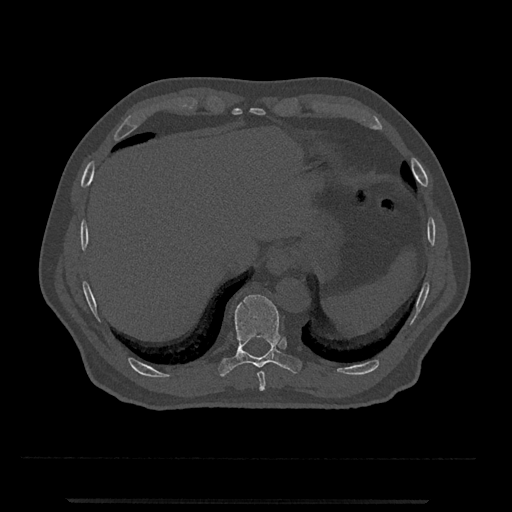
CT including the spine, one axial slice; position 526 of 797 along the scan axis; bone window (W 1800 / L 400 HU); 0.5 mm slice thickness; 512 × 512 image matrix, field of view 419 × 419 mm. Patient: male, 63 years. Case-level facts recorded for this patient, not image findings: primary cancer: prostate.
Outlined on this slice (semi-automatically segmented with operator editing):
- T10 vertebra: bounding box [x1, y1, x2, y2] px = [218, 295, 302, 377]
- T9 vertebra: [257, 371, 266, 391]